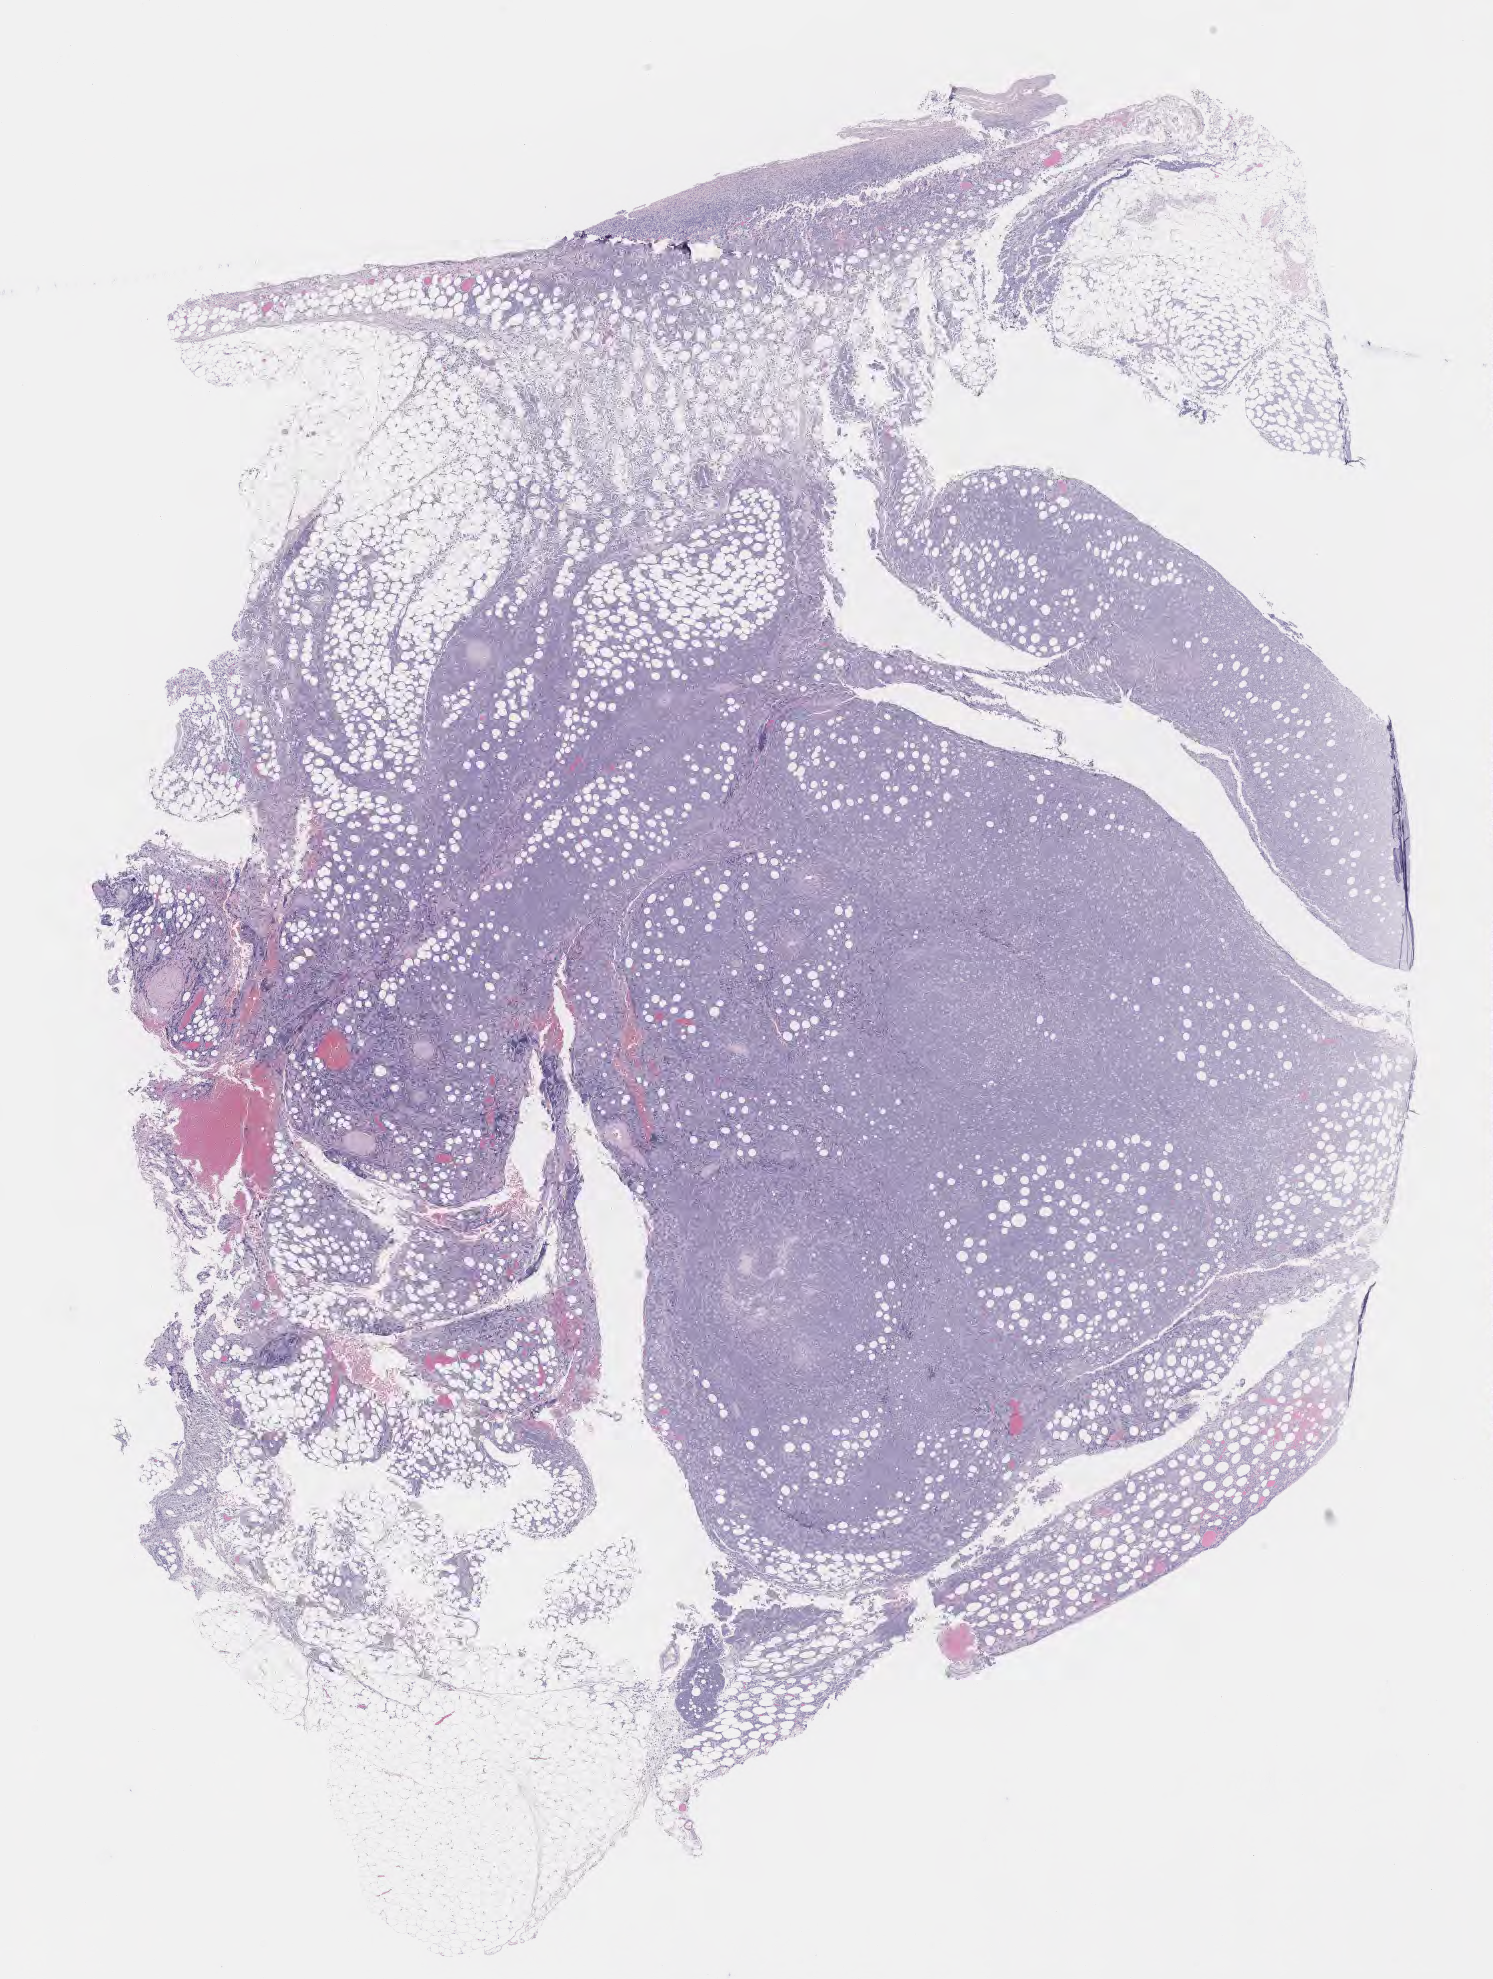
Hematoxylin and eosin (H&E) whole-slide image — a low-resolution overview of the entire scanned area, about 12.1 x 16.0 mm; specimen: tumor tissue; anatomic site: small intestine. Patient: male, age 19 years.
Diagnosis: Burkitt lymphoma, NOS.